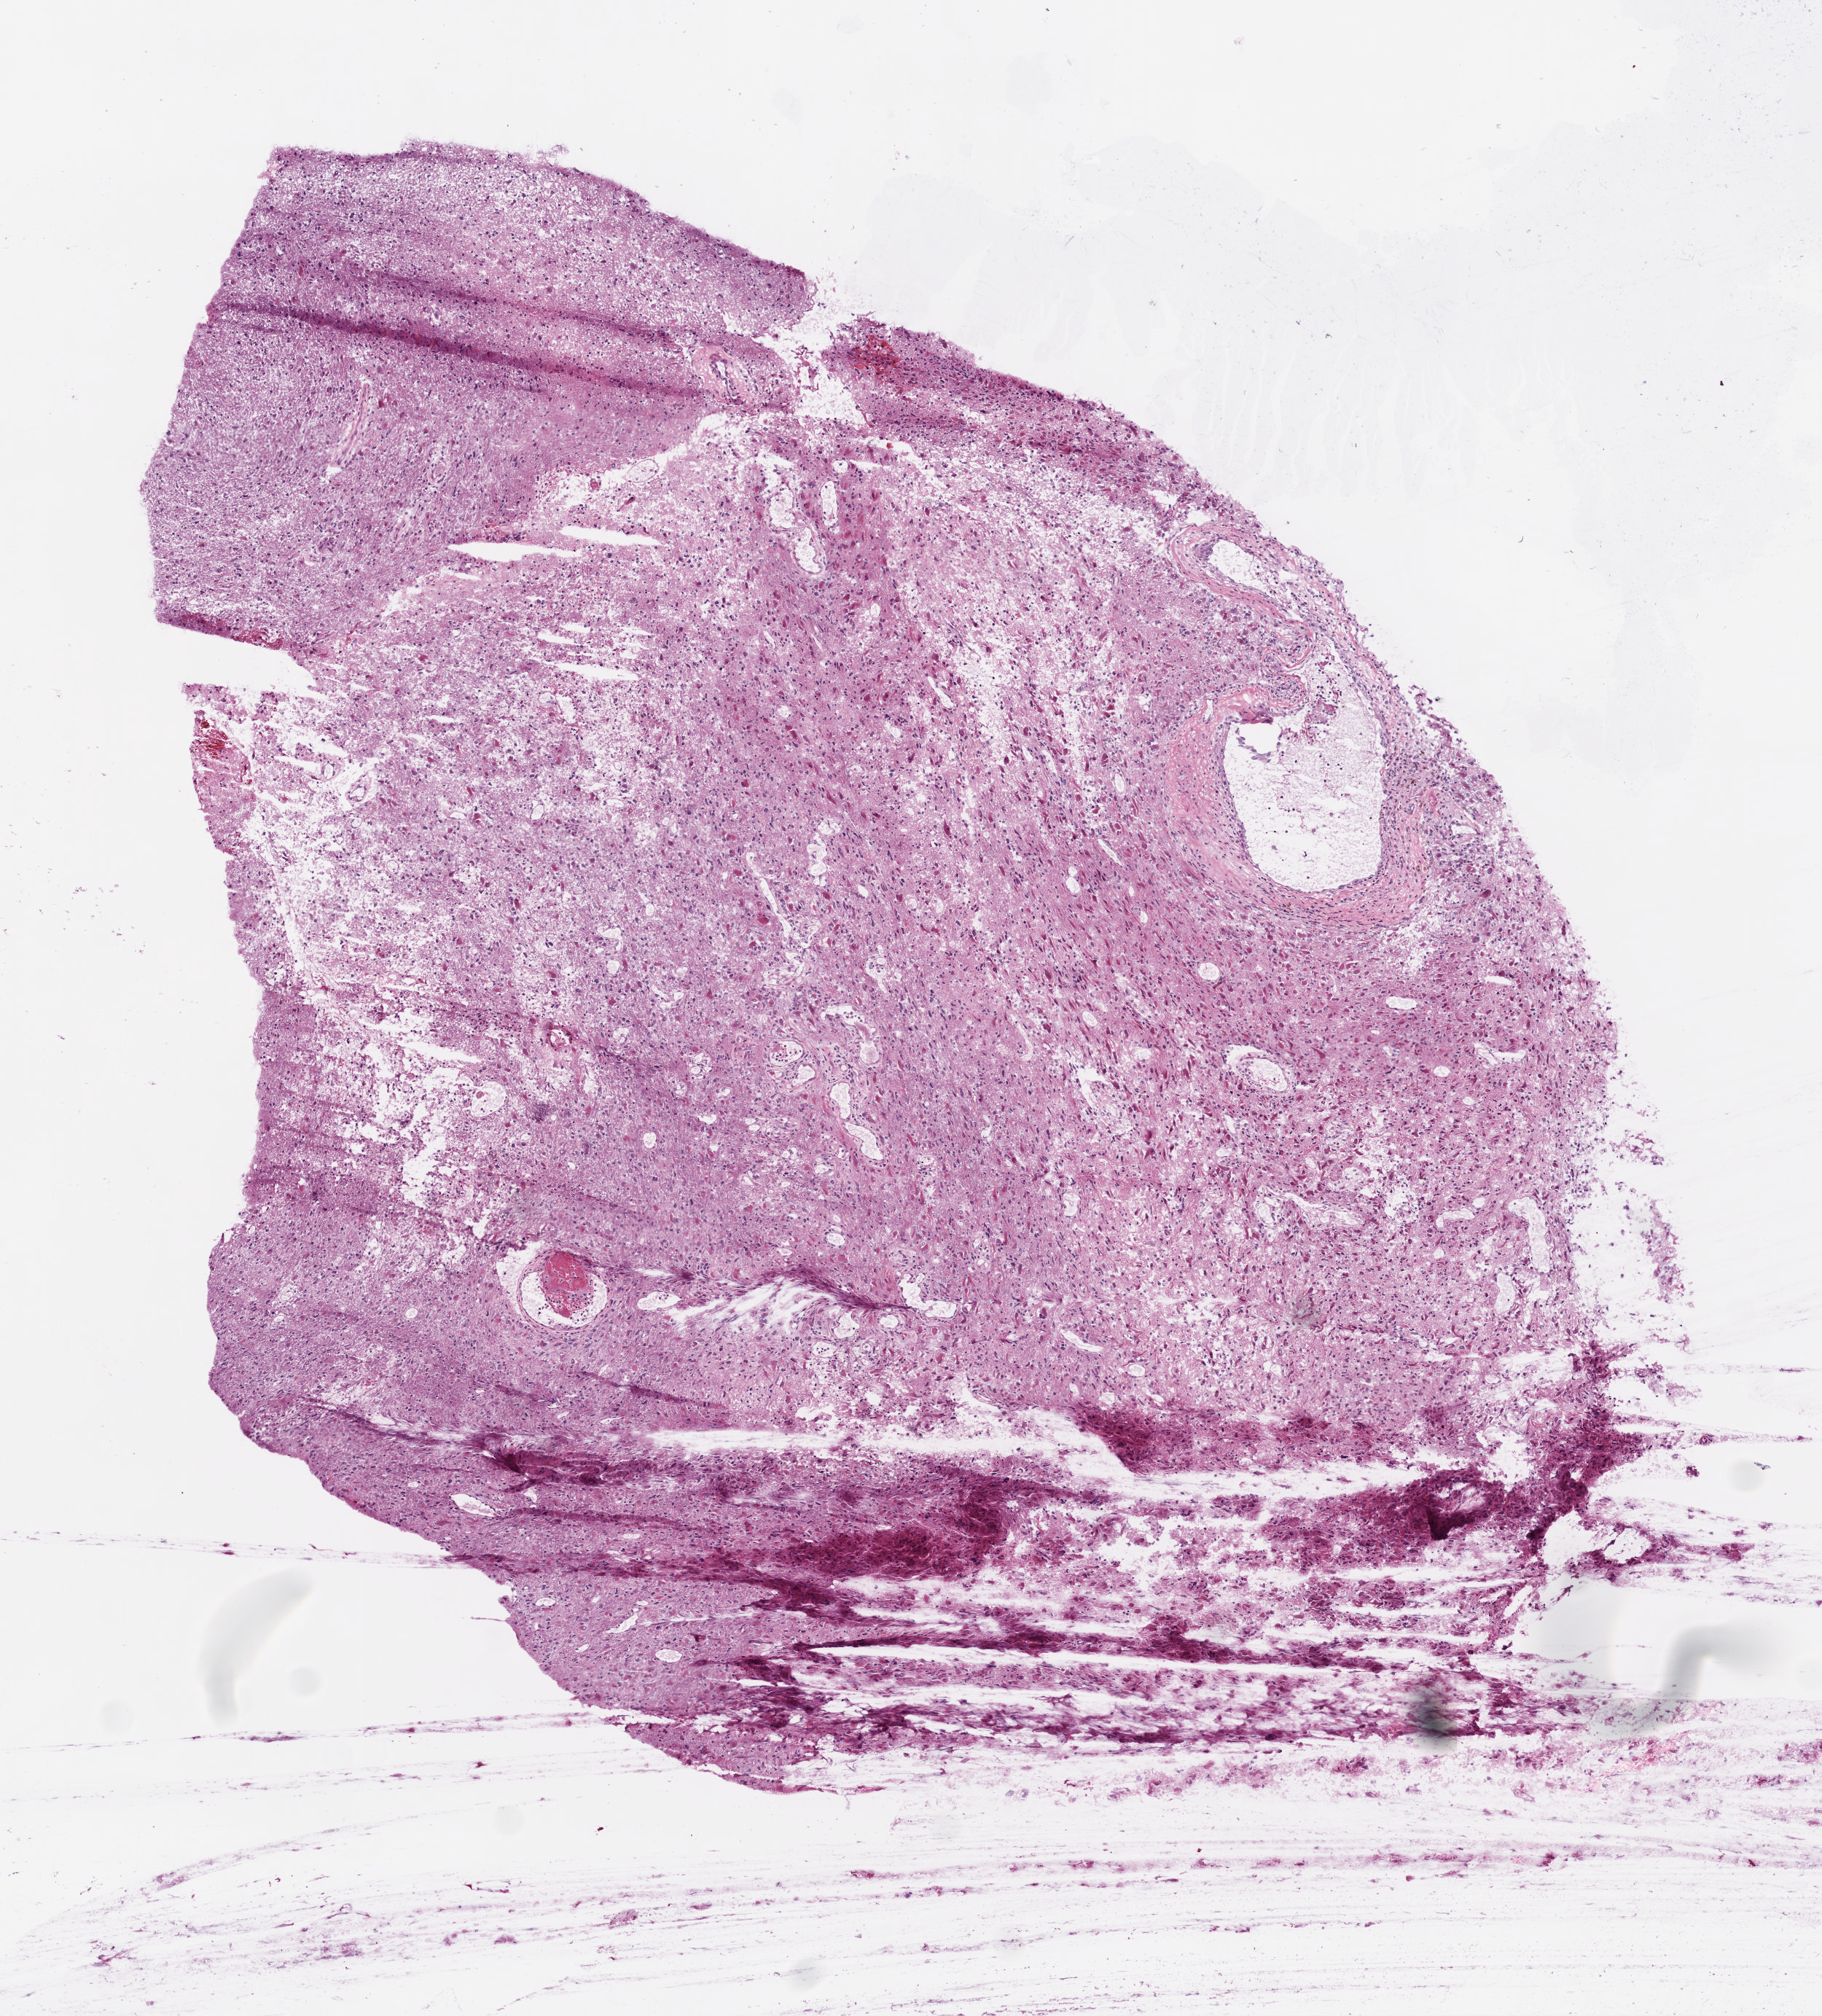
Hematoxylin and eosin (H&E) stained whole-slide image — a low-resolution overview of the entire scanned area, about 5.0 x 5.5 mm. Frozen section from the top of the tissue portion. Sample: primary tumour, brain. Patient: male, age at initial diagnosis 56 years. Composition of this section per pathologist review: tumour cells 99%, tumour nuclei 80%, normal cells 0%, stromal cells 0%, necrosis 1%.
• pathologic diagnosis: Glioblastoma